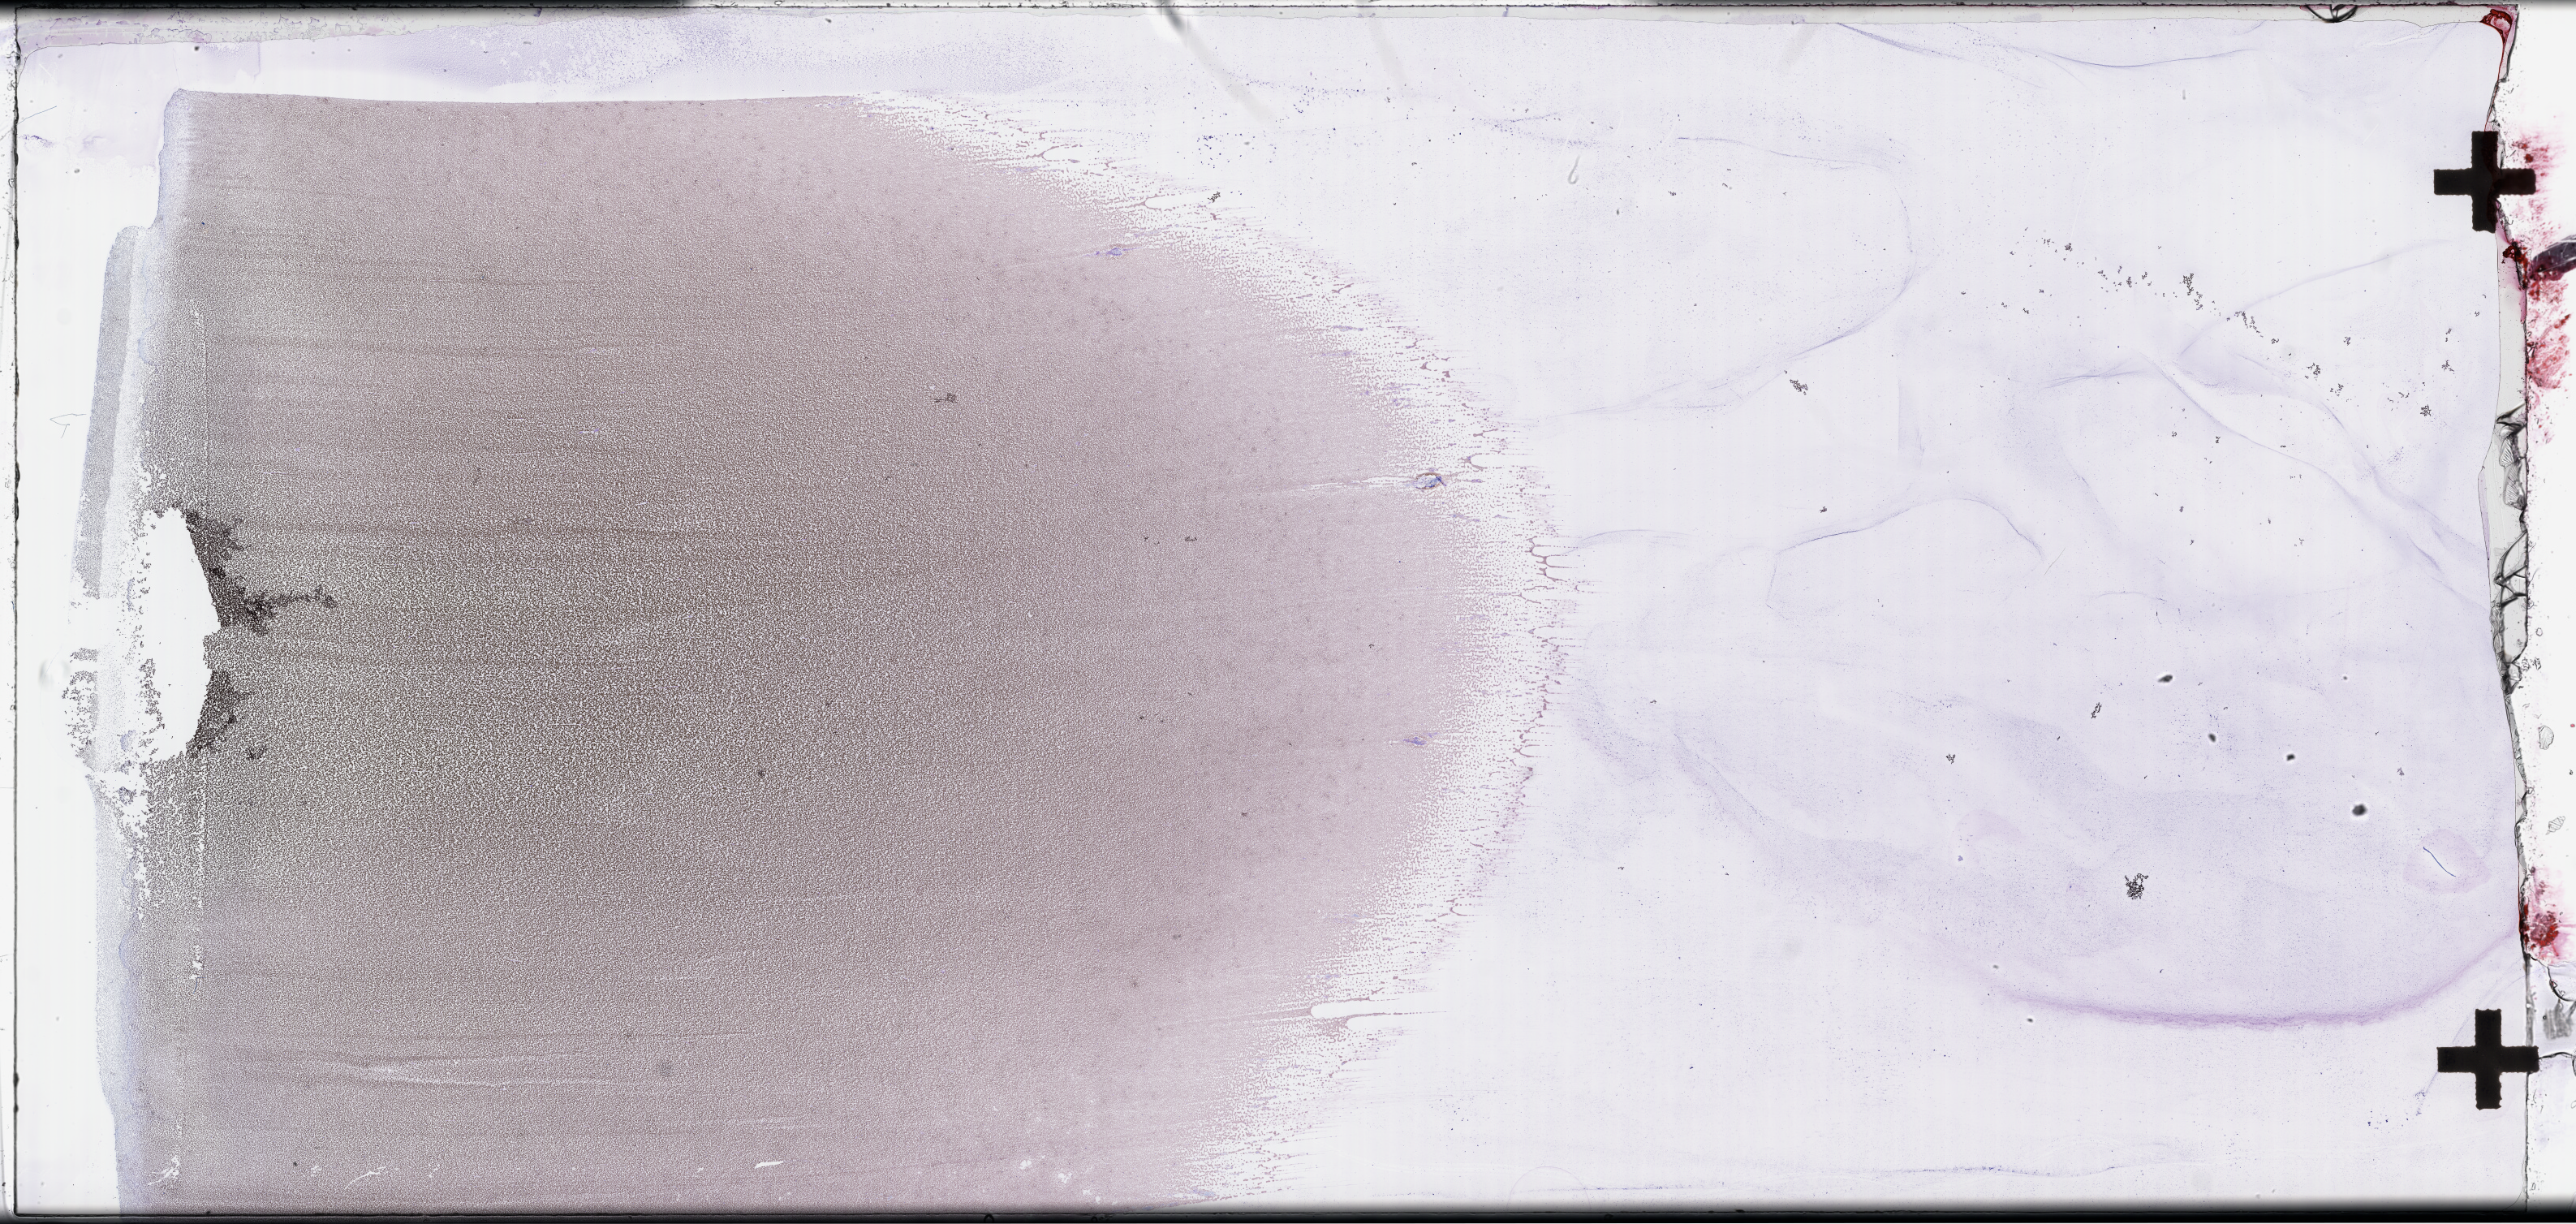
Whole-slide image of a whole blood smear, Wright–Giemsa stain — whole scanned area (about 51.3 x 24.4 mm) shown as a low-resolution overview. Patient sex: male.
- from a patient with: Plasma Cell Myeloma